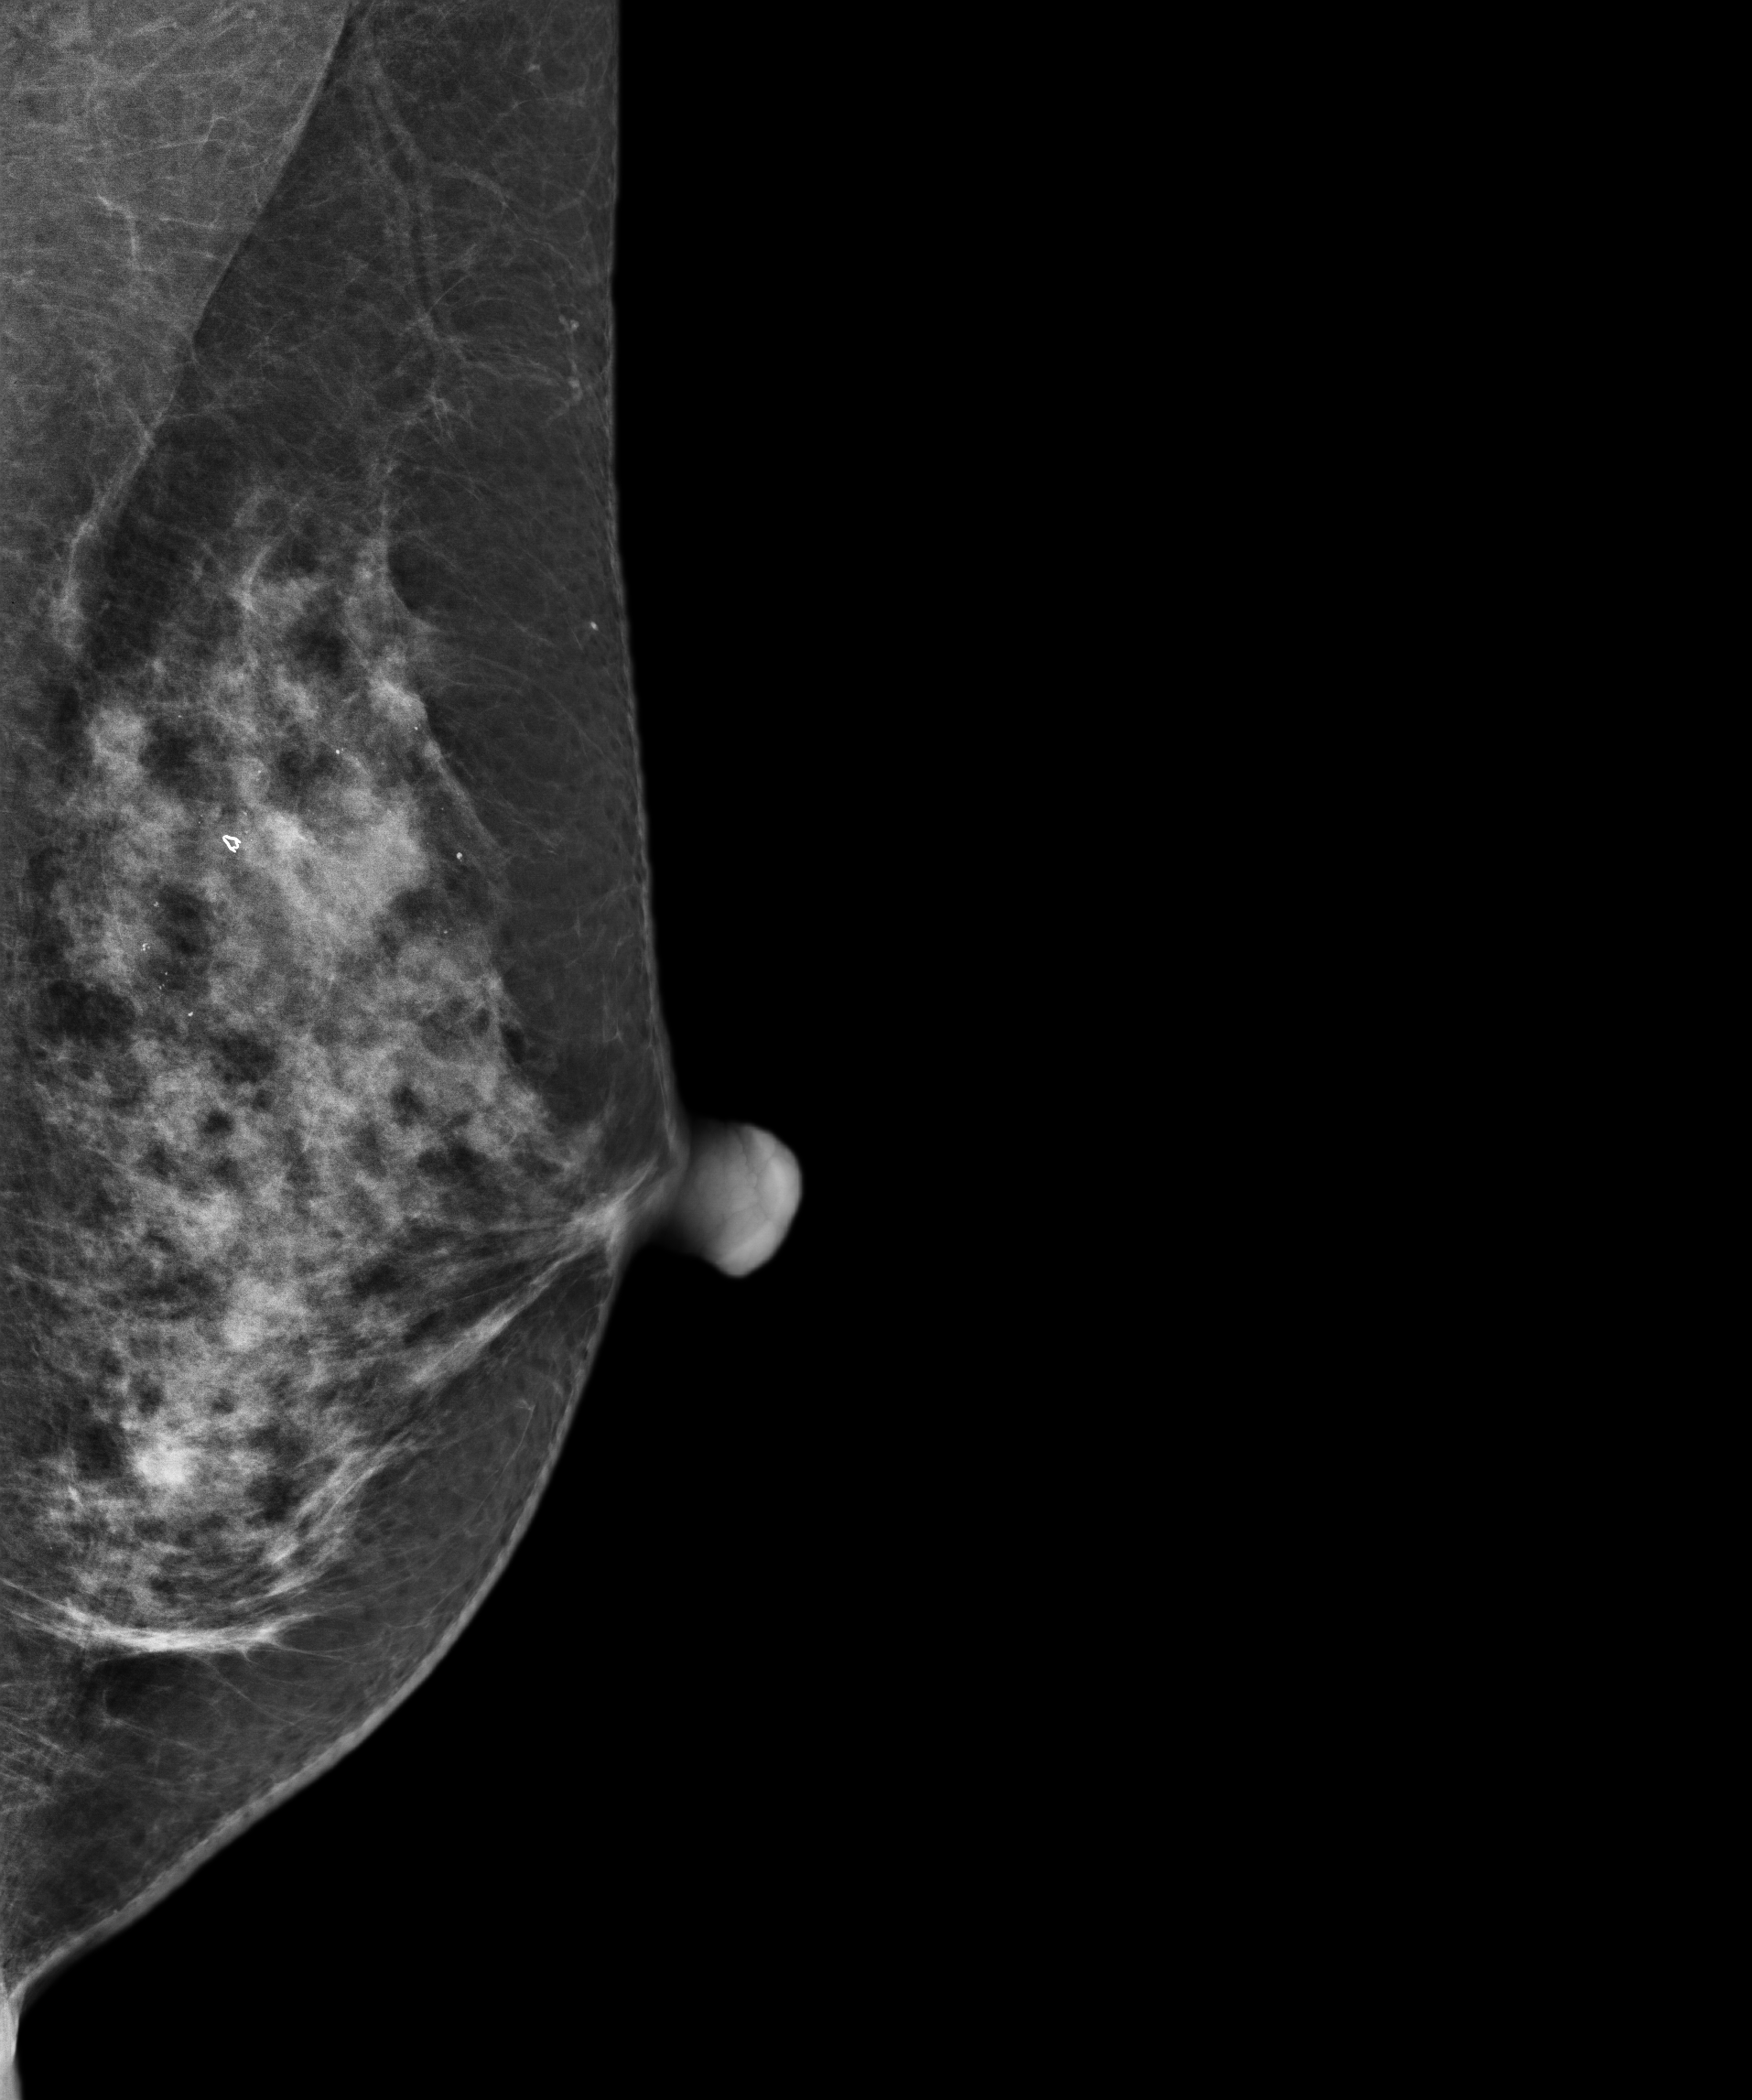
Annual screening mammography examination.
Image type: full-field digital mammogram. Breast: left. Projection: MLO view.